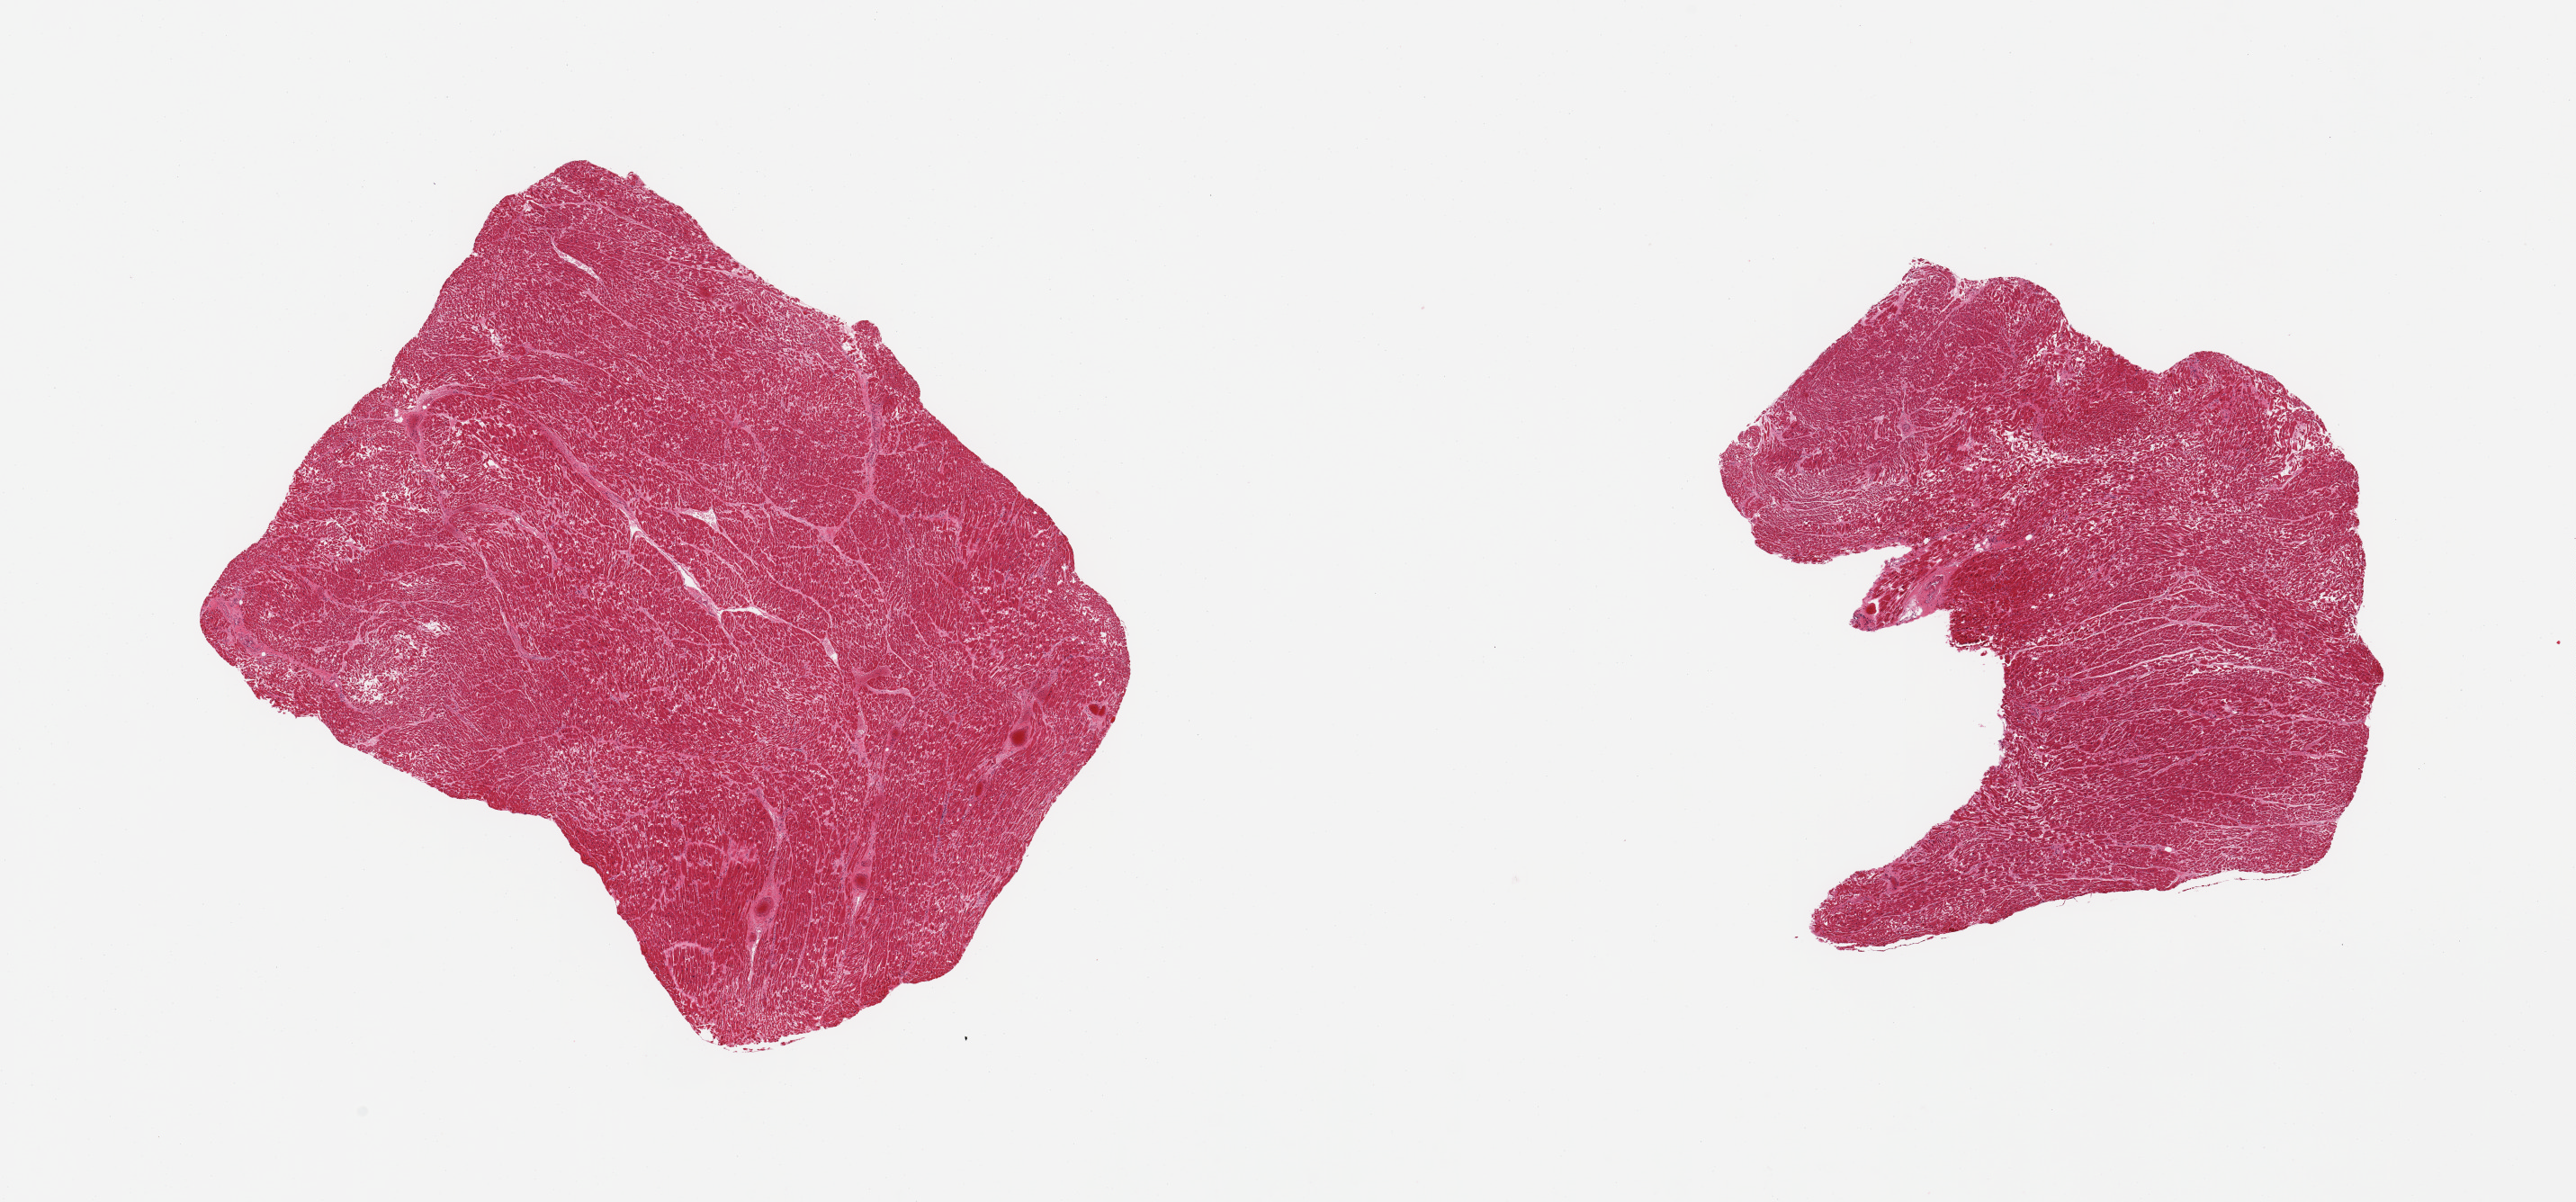
Whole-slide image, H&E stain, brightfield, whole scanned area (about 22.6 x 10.6 mm, from a 20x scan) shown as a low-resolution overview, PAXgene-fixed, paraffin-embedded tissue, sampled site (target tissue): heart, donor tissue sample. Donor: female.
- reviewer comment on this tissue sample: 2 pieces